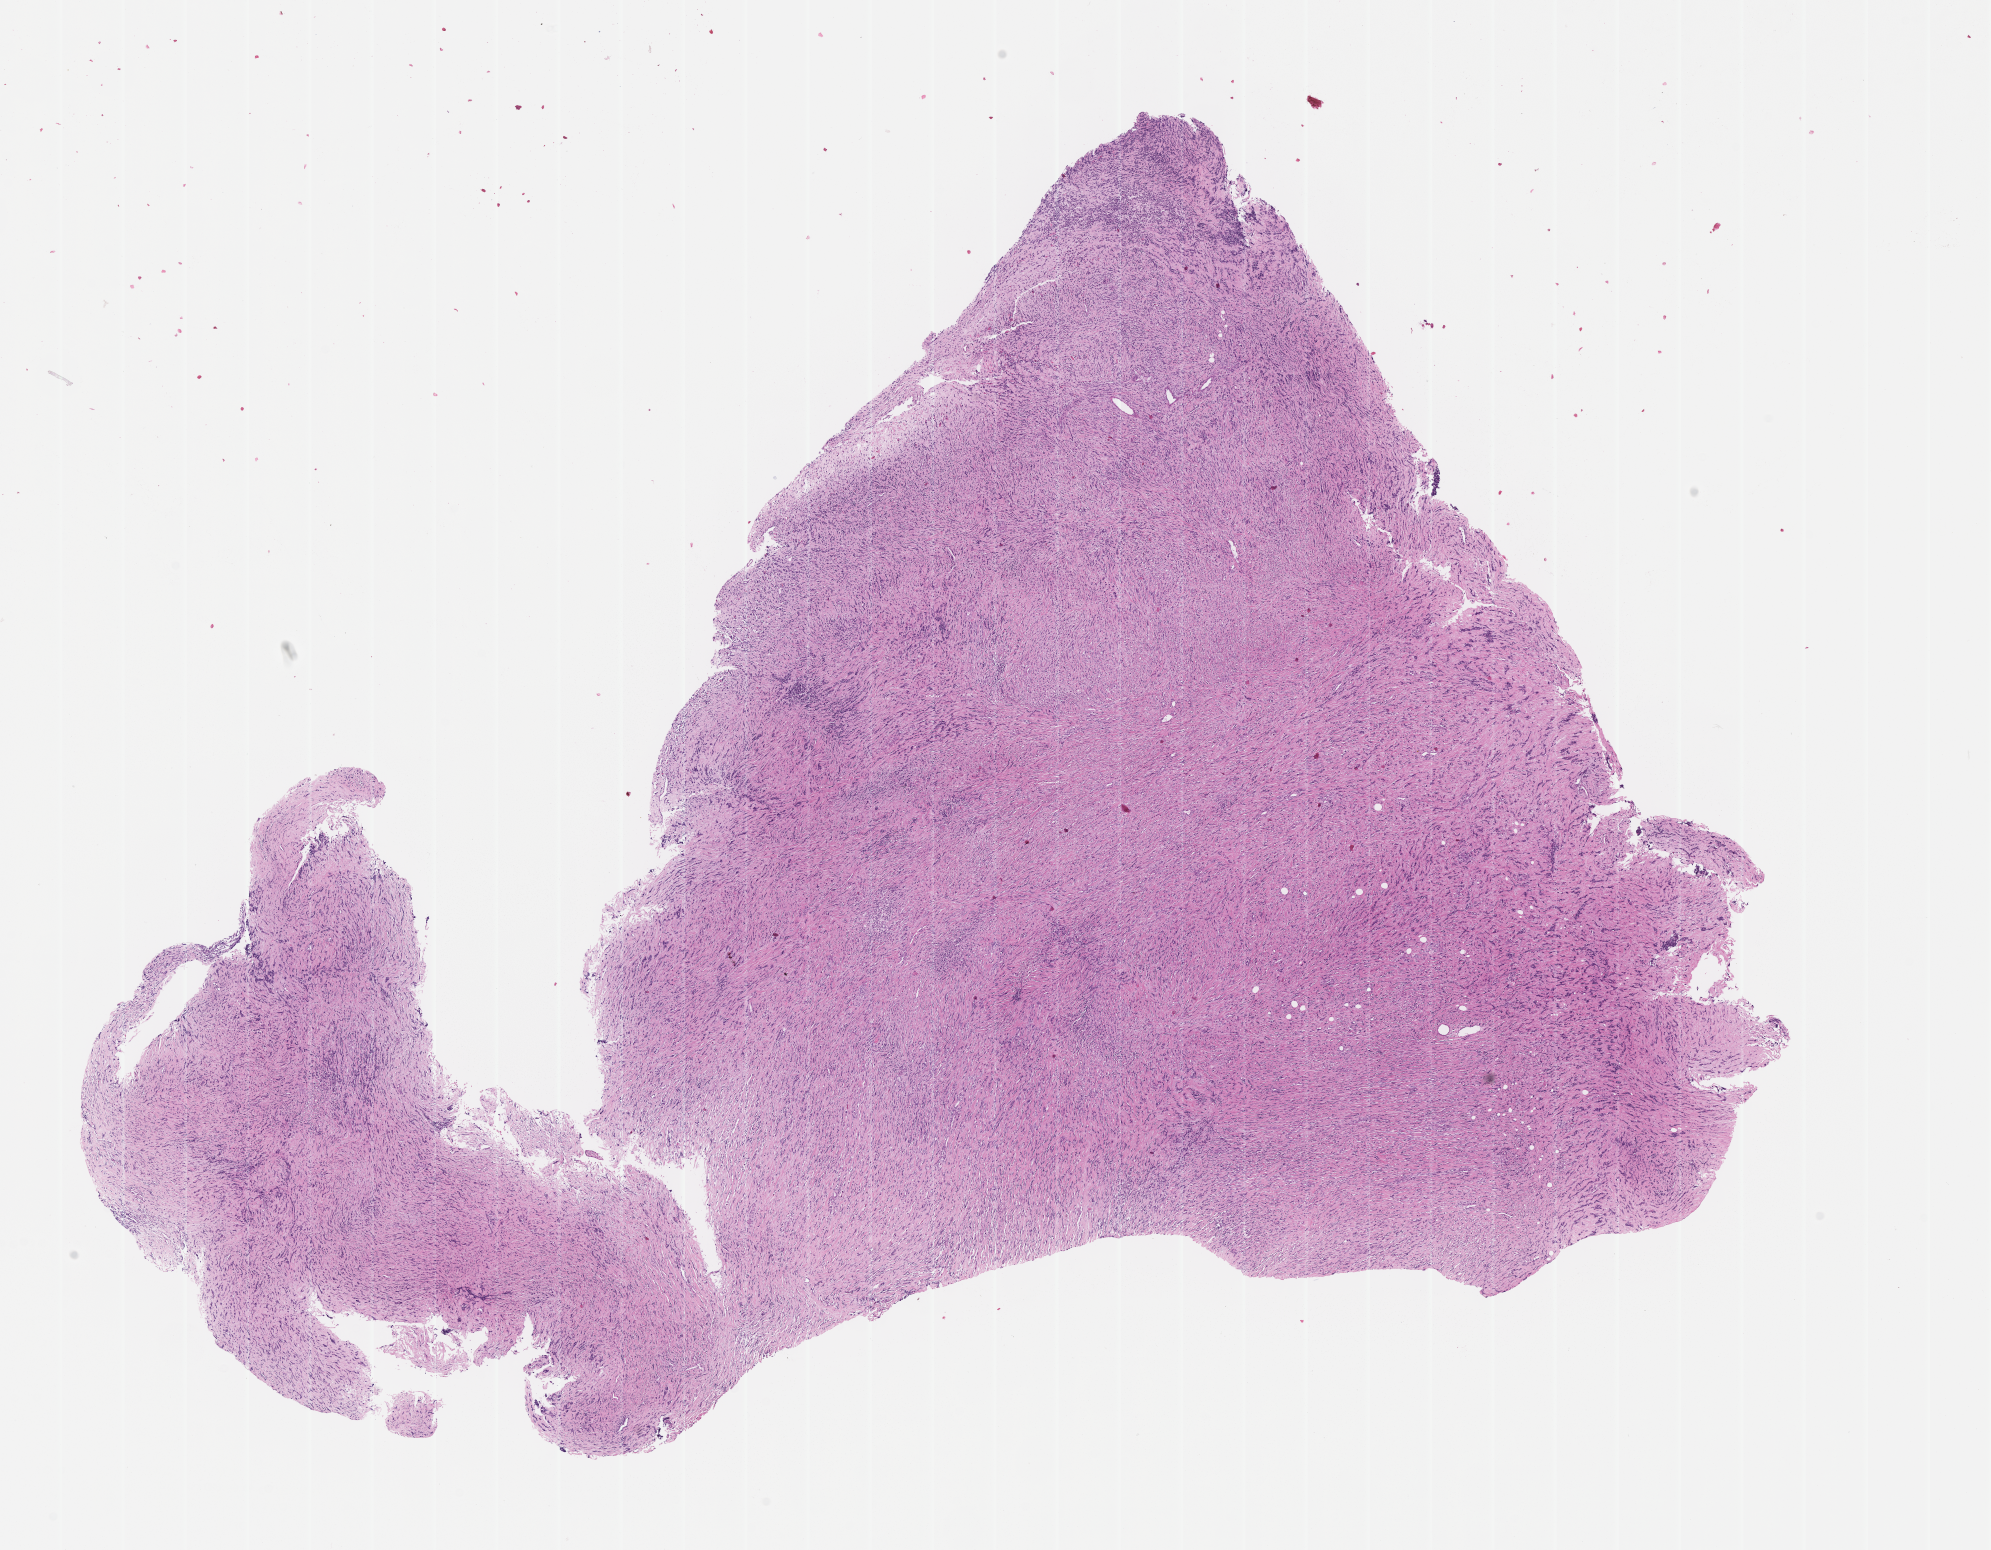
Digitized haematoxylin and eosin-stained section of tumor tissue — low-resolution overview of the scanned area, about 16.1 x 12.5 mm. FFPE section. Site: soft tissue, cheek-right. Female patient, age at diagnosis 20.0 years.
Stage (as recorded): 3. Diagnosis: rhabdomyosarcoma; histological classification: embryonal rhabdomyosarcoma. Metastatic status at presentation (as recorded): non-metastatic.